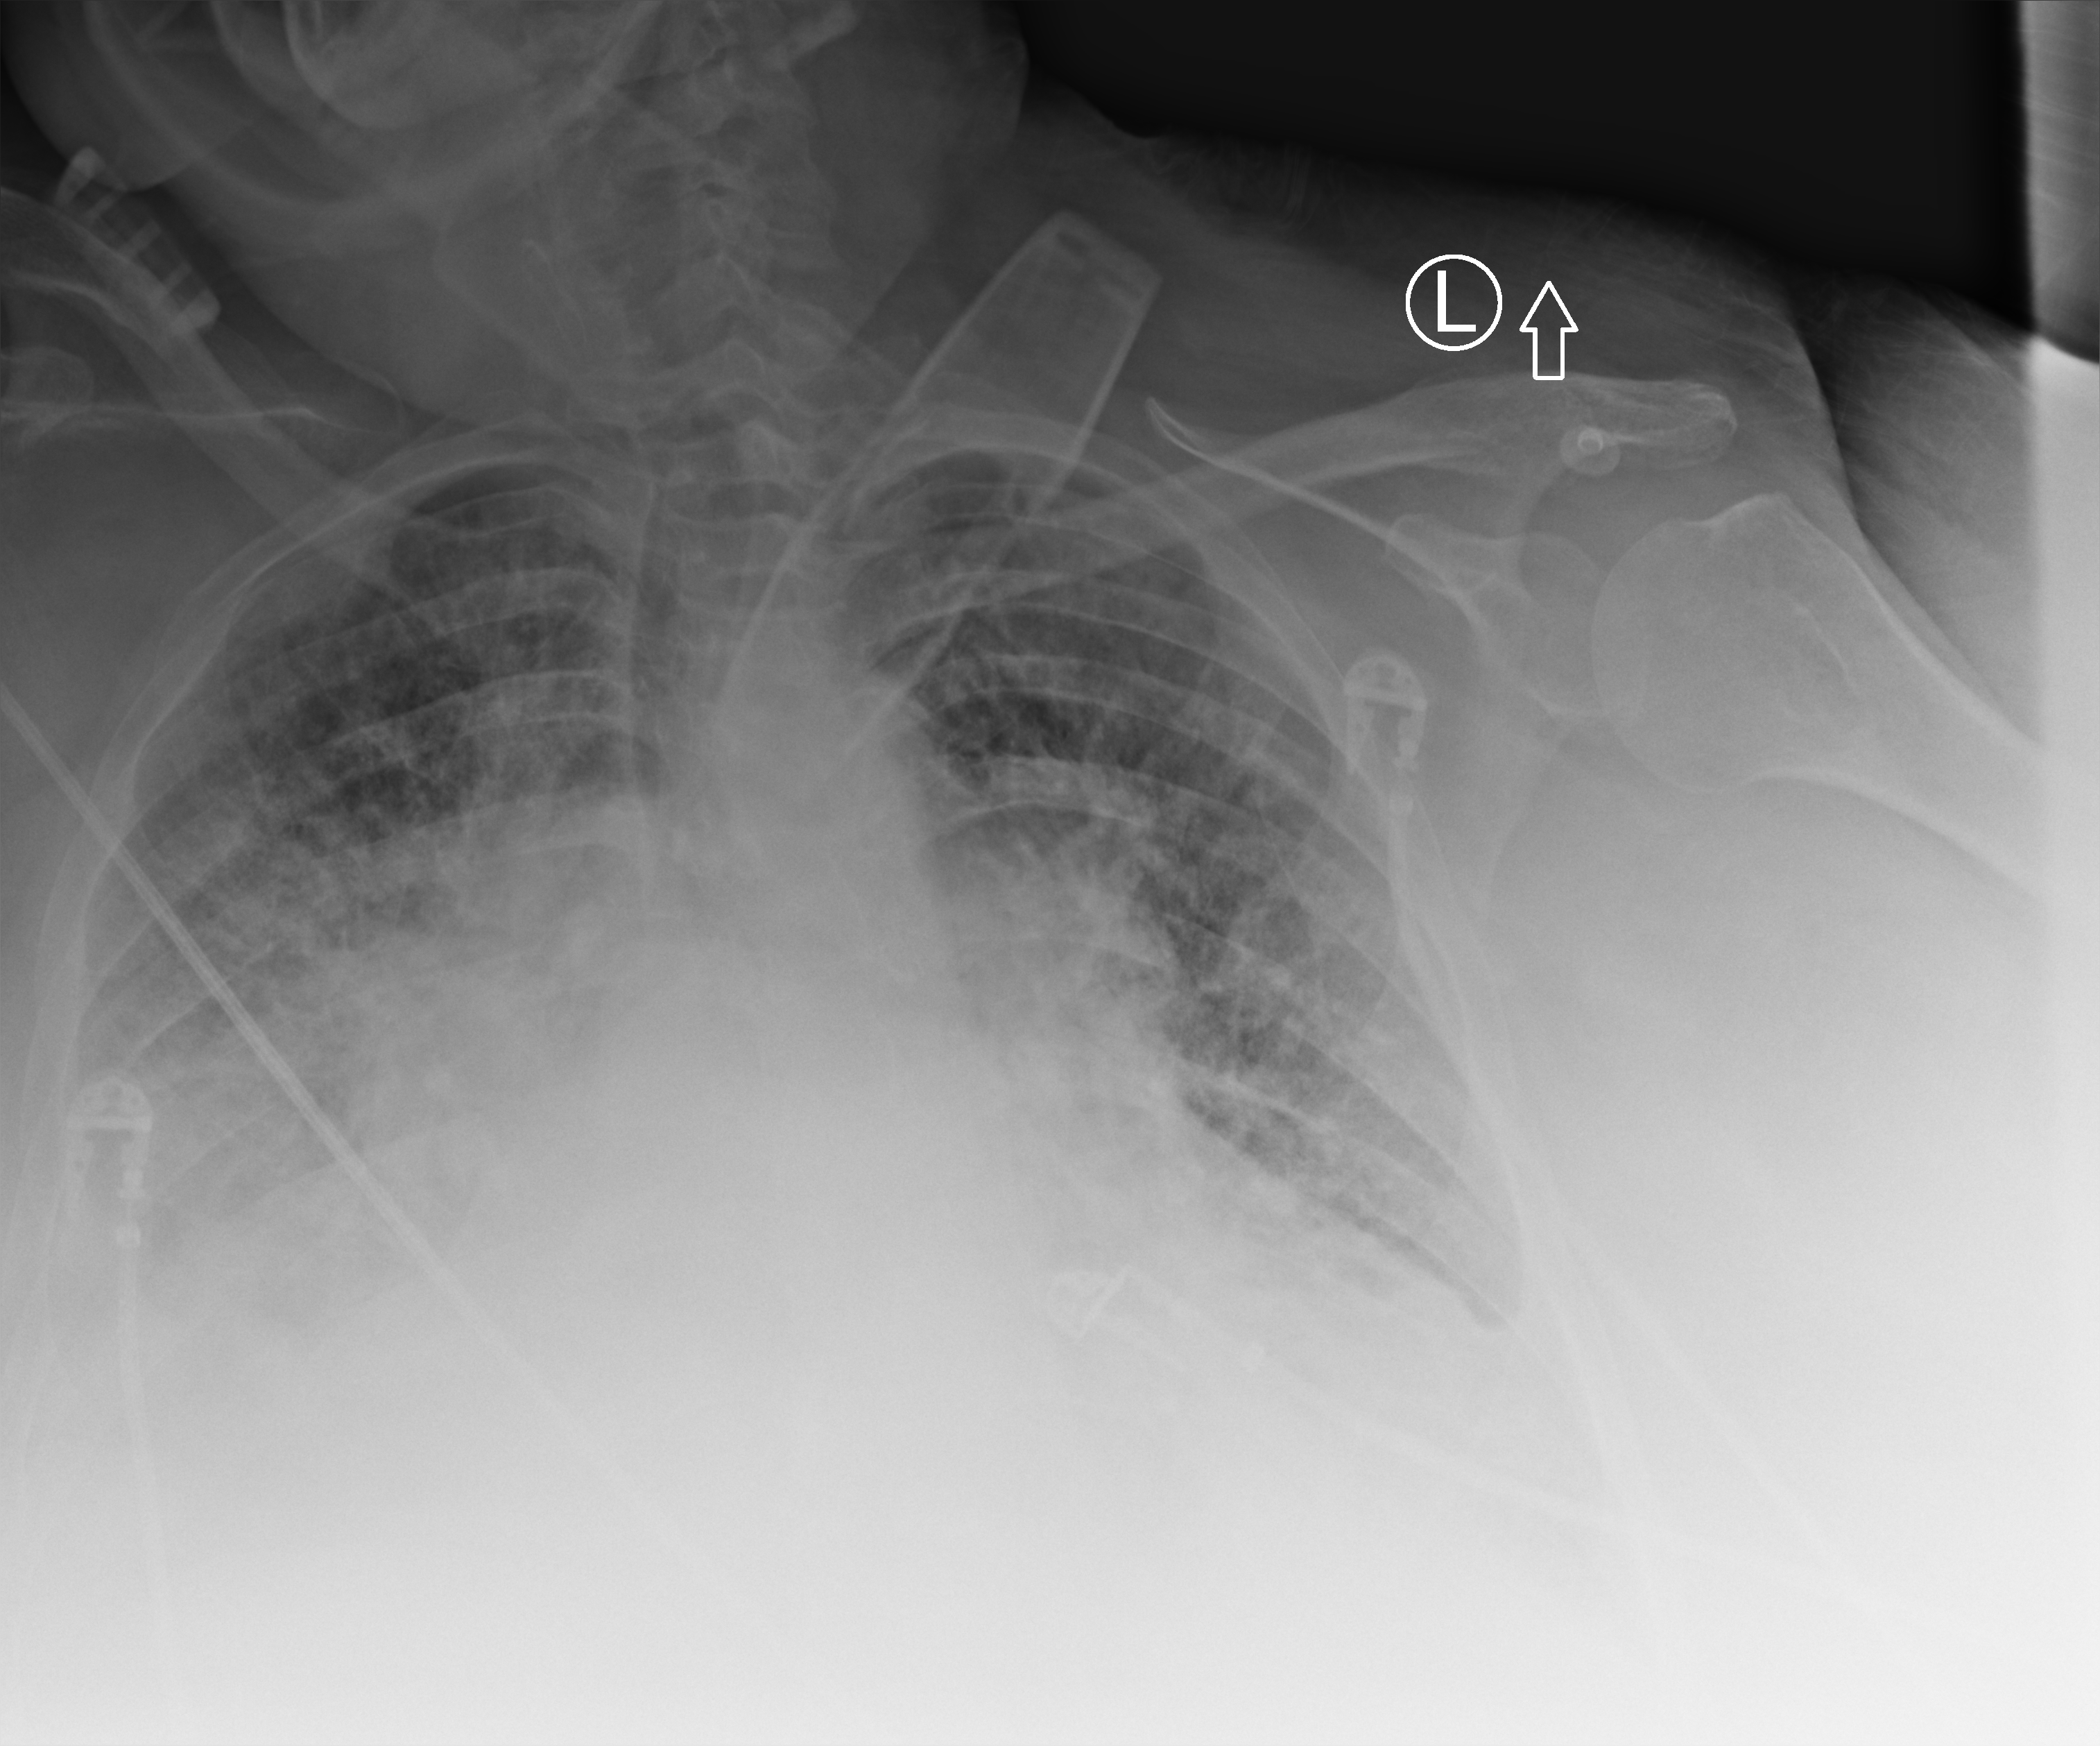
Chest X-ray (portable); anteroposterior (AP) projection. Patient hospitalised with COVID-19; female, aged 60–74 years.
Admission-level facts for this patient (not findings on this image; timing relative to this image not recorded):
- mechanically ventilated during this hospital stay: yes